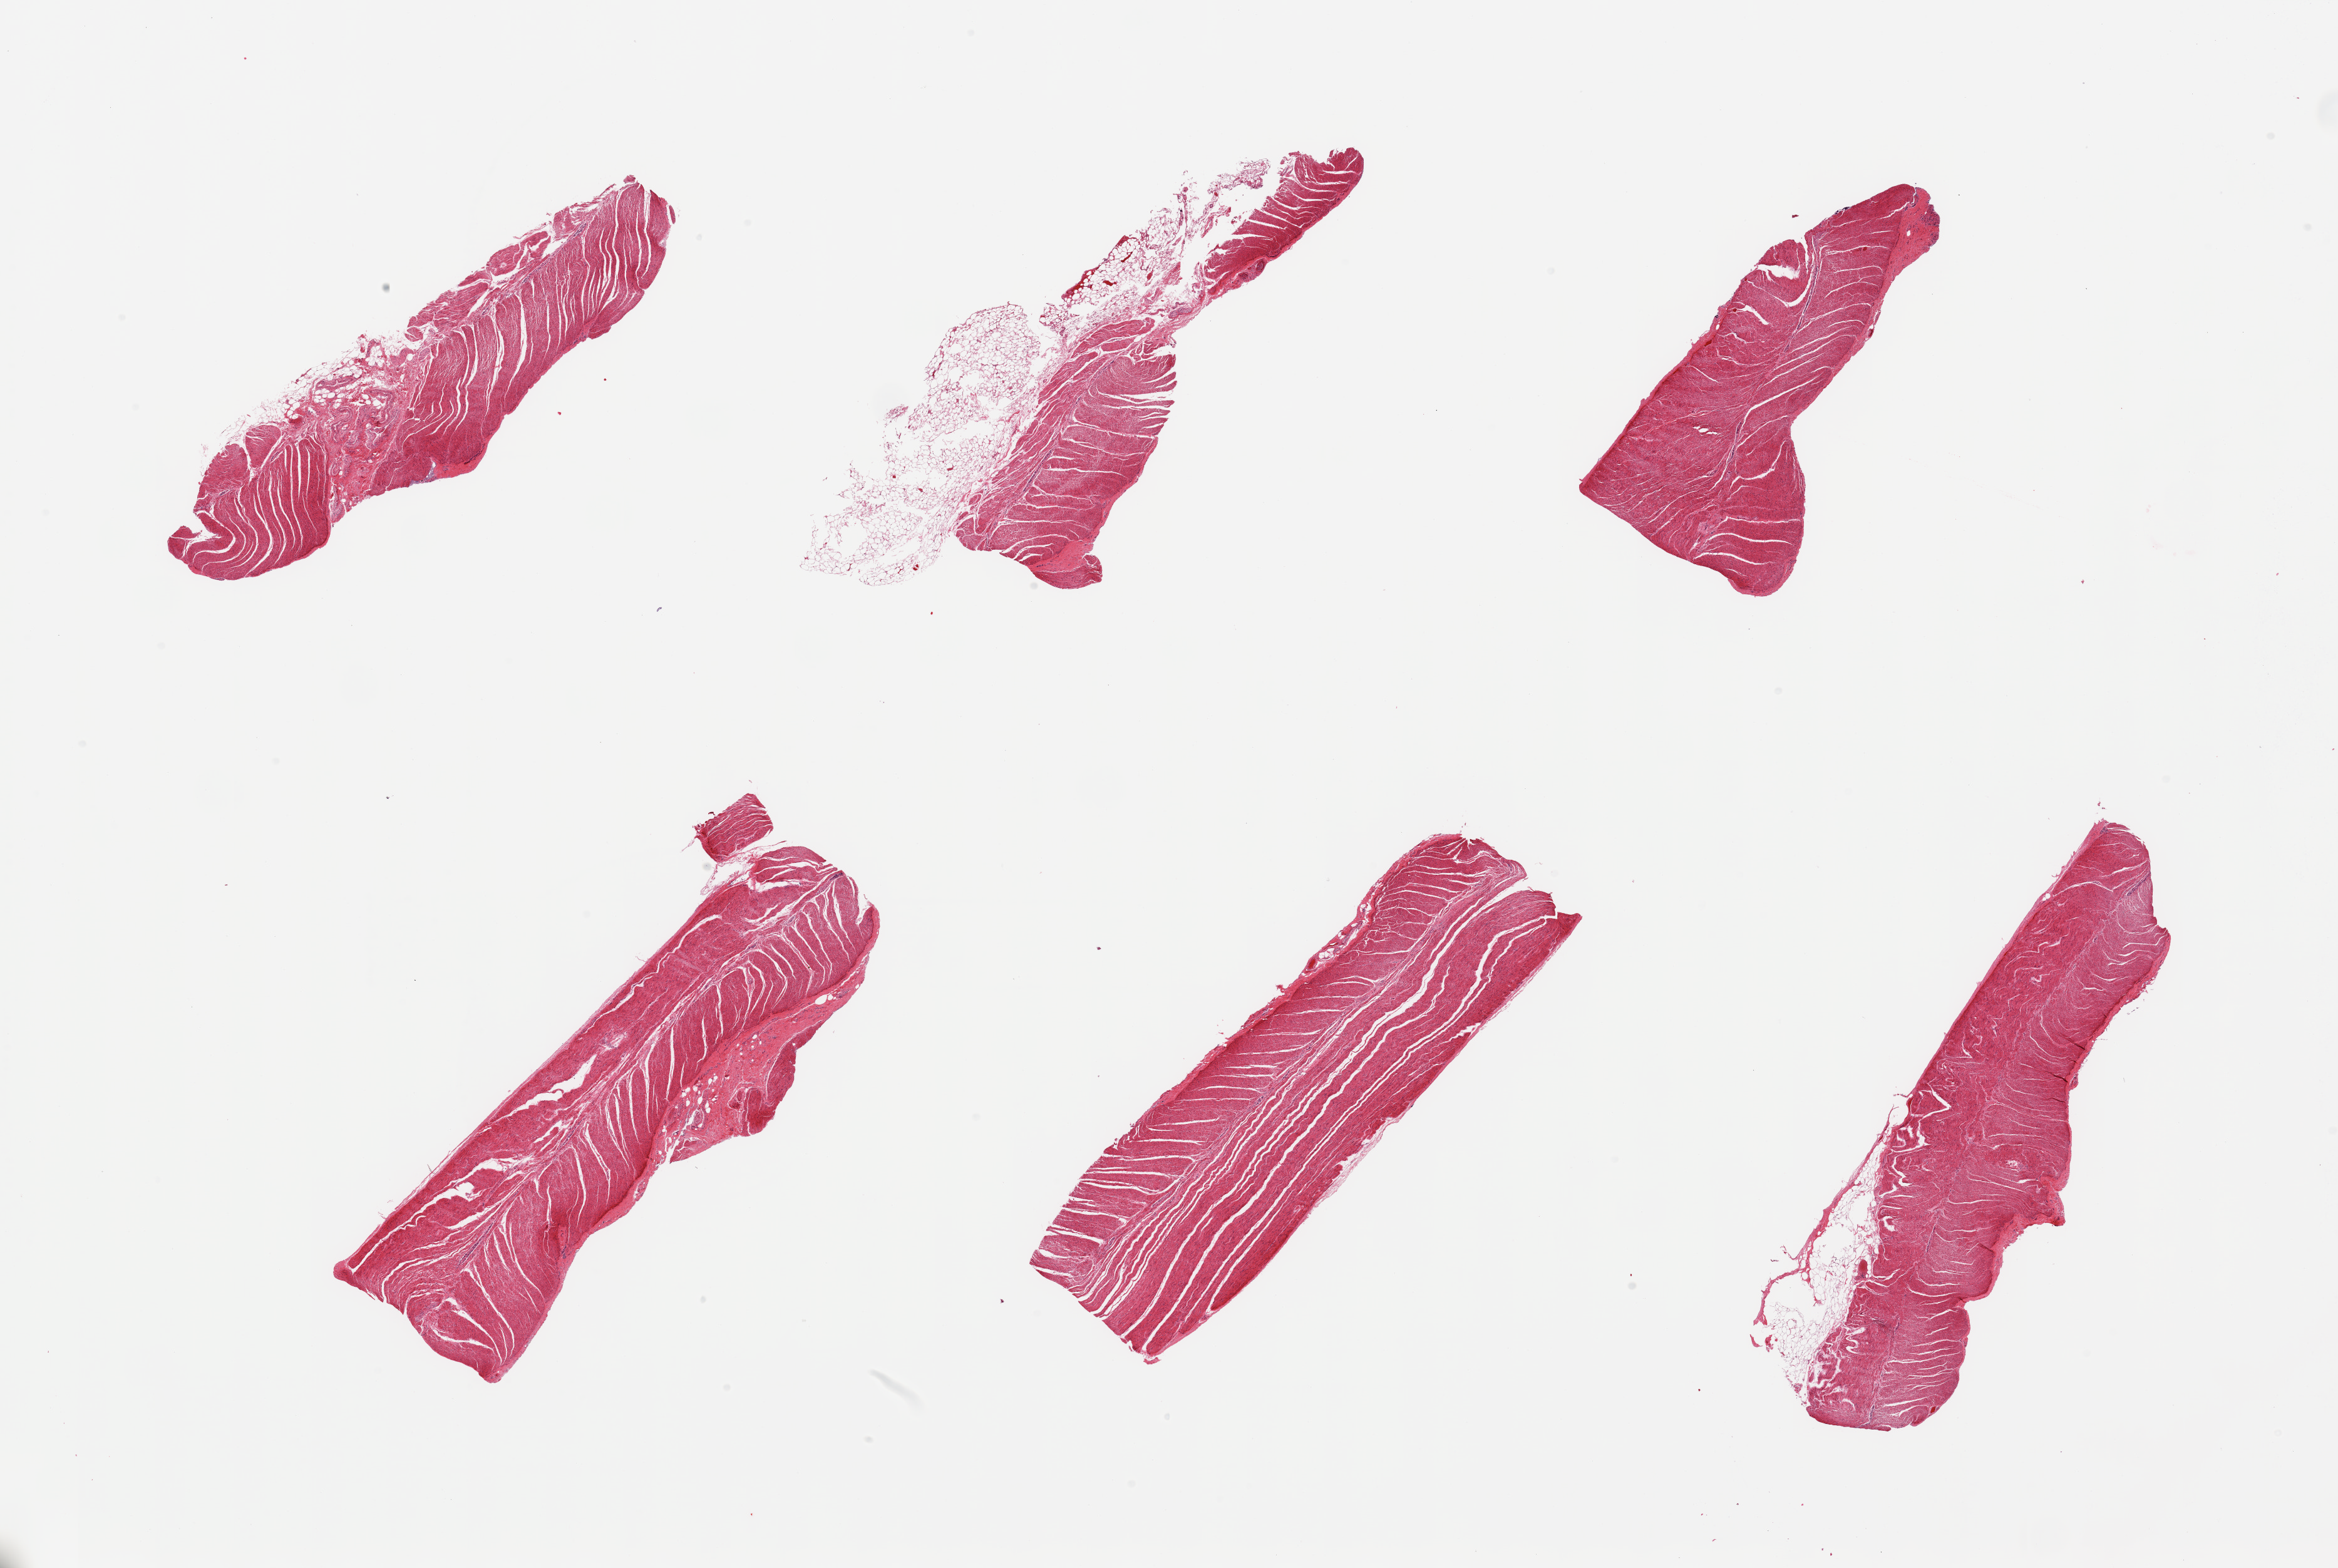
Whole-slide image, haematoxylin and eosin stain — shown as a low-resolution overview of the whole scanned area (about 29.5 x 19.8 mm, acquisition: 20x scan), PAXgene-fixed paraffin-embedded (PFPE) section, target tissue: sigmoid colon, tissue donor sample. Donor: male.
• review note (as recorded): 6 pieces, confirmed target muscularis